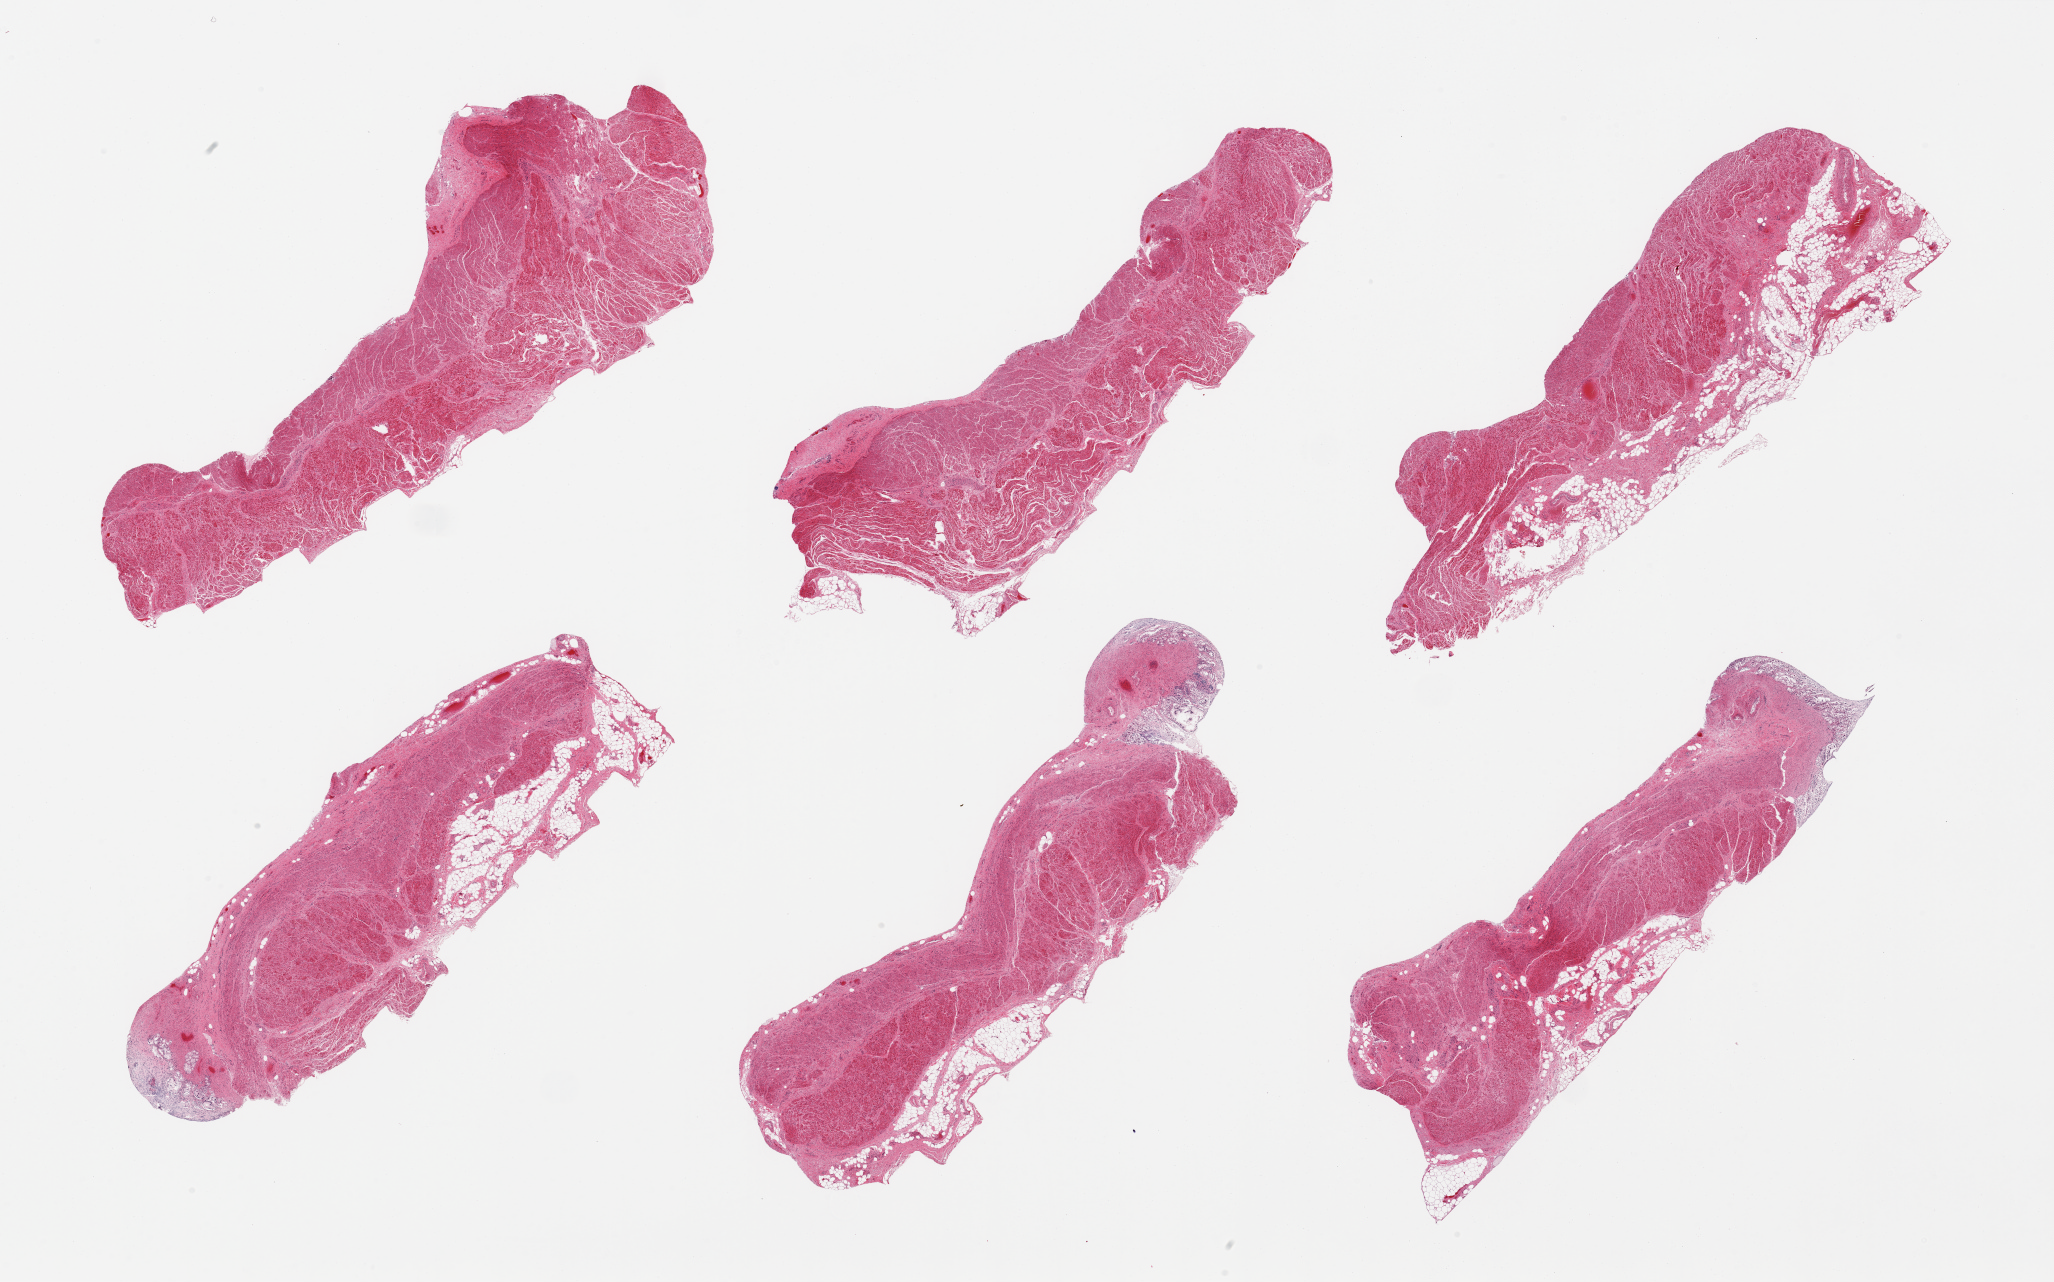
H&E whole-slide image, brightfield — a low-resolution overview of the entire scanned area, about 32.5 x 20.3 mm. PAXgene-fixed, paraffin-embedded tissue. Sampled site (target tissue): gastroesophageal junction. Donor tissue sample. Donor: male.
Review note (as recorded): 6 pieces; two pieces contain small foci of autolysed (grade 3) mucosa; muscularis intact; adherent fat up to 2.4mm.